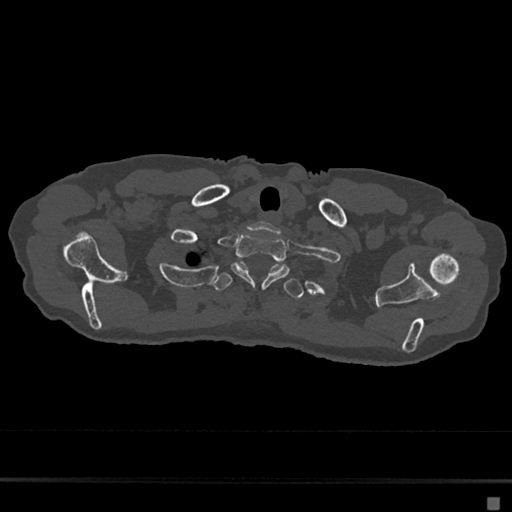
CT including the spine, one axial slice. Position 600 of 797 along the scan axis. Reconstruction kernel Br40s/3. 120 kVp. Bone window (W 1800 / L 400 HU). 0.5 mm slice thickness. 512 × 512 image matrix, field of view 360 × 360 mm. Patient: female, 68 years. From the clinical record (not read from this slice): primary cancer: renal.
Annotated regions visible in this slice (semi-automatically segmented with operator editing):
- T1 vertebra: box from (x=231, y=235) to (x=290, y=289) px
- T2 vertebra: (x=212, y=264)–(x=304, y=299)